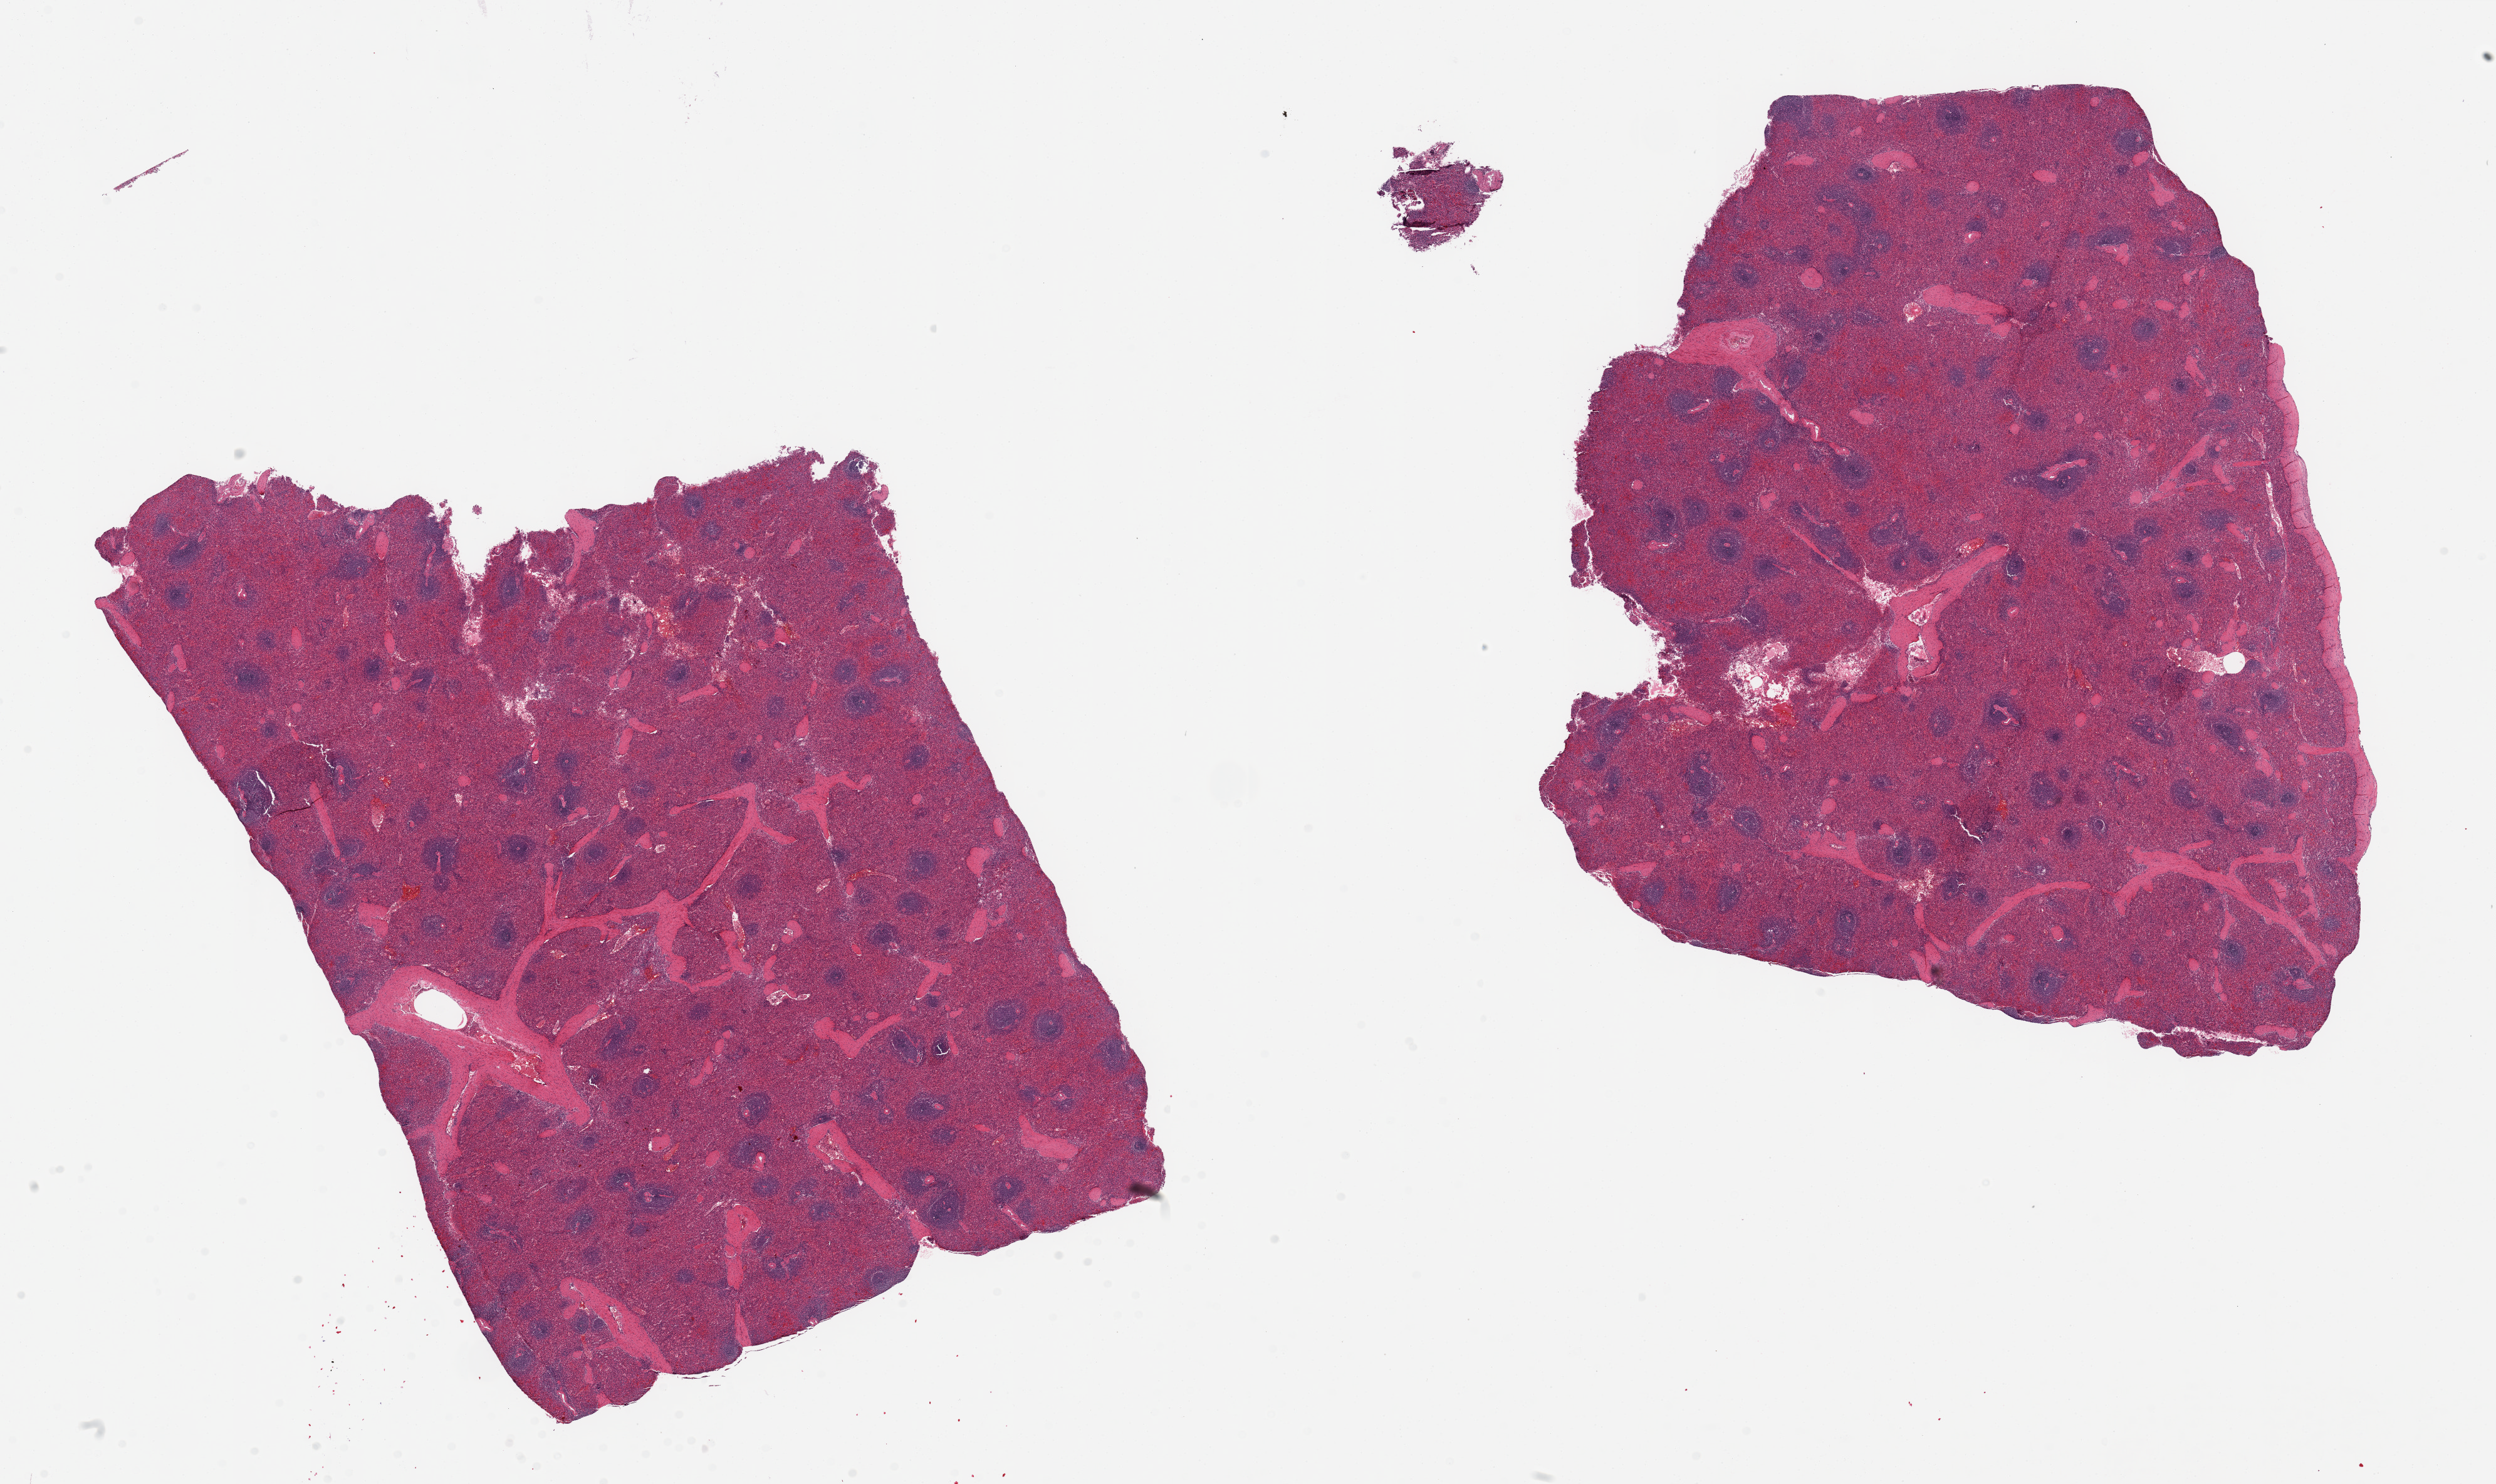
Digitized hematoxylin and eosin (H&E)-stained section — whole scanned area (about 31.5 x 18.7 mm, from a 20x scan) shown as a low-resolution overview. PAXgene-fixed, paraffin-embedded tissue. Target tissue: spleen. Tissue donor sample. Donor: male.
Pathologist's review note for this sample: 2 pieces, 13x10 & 12x10.5mm; mild congestion; well-preserved.